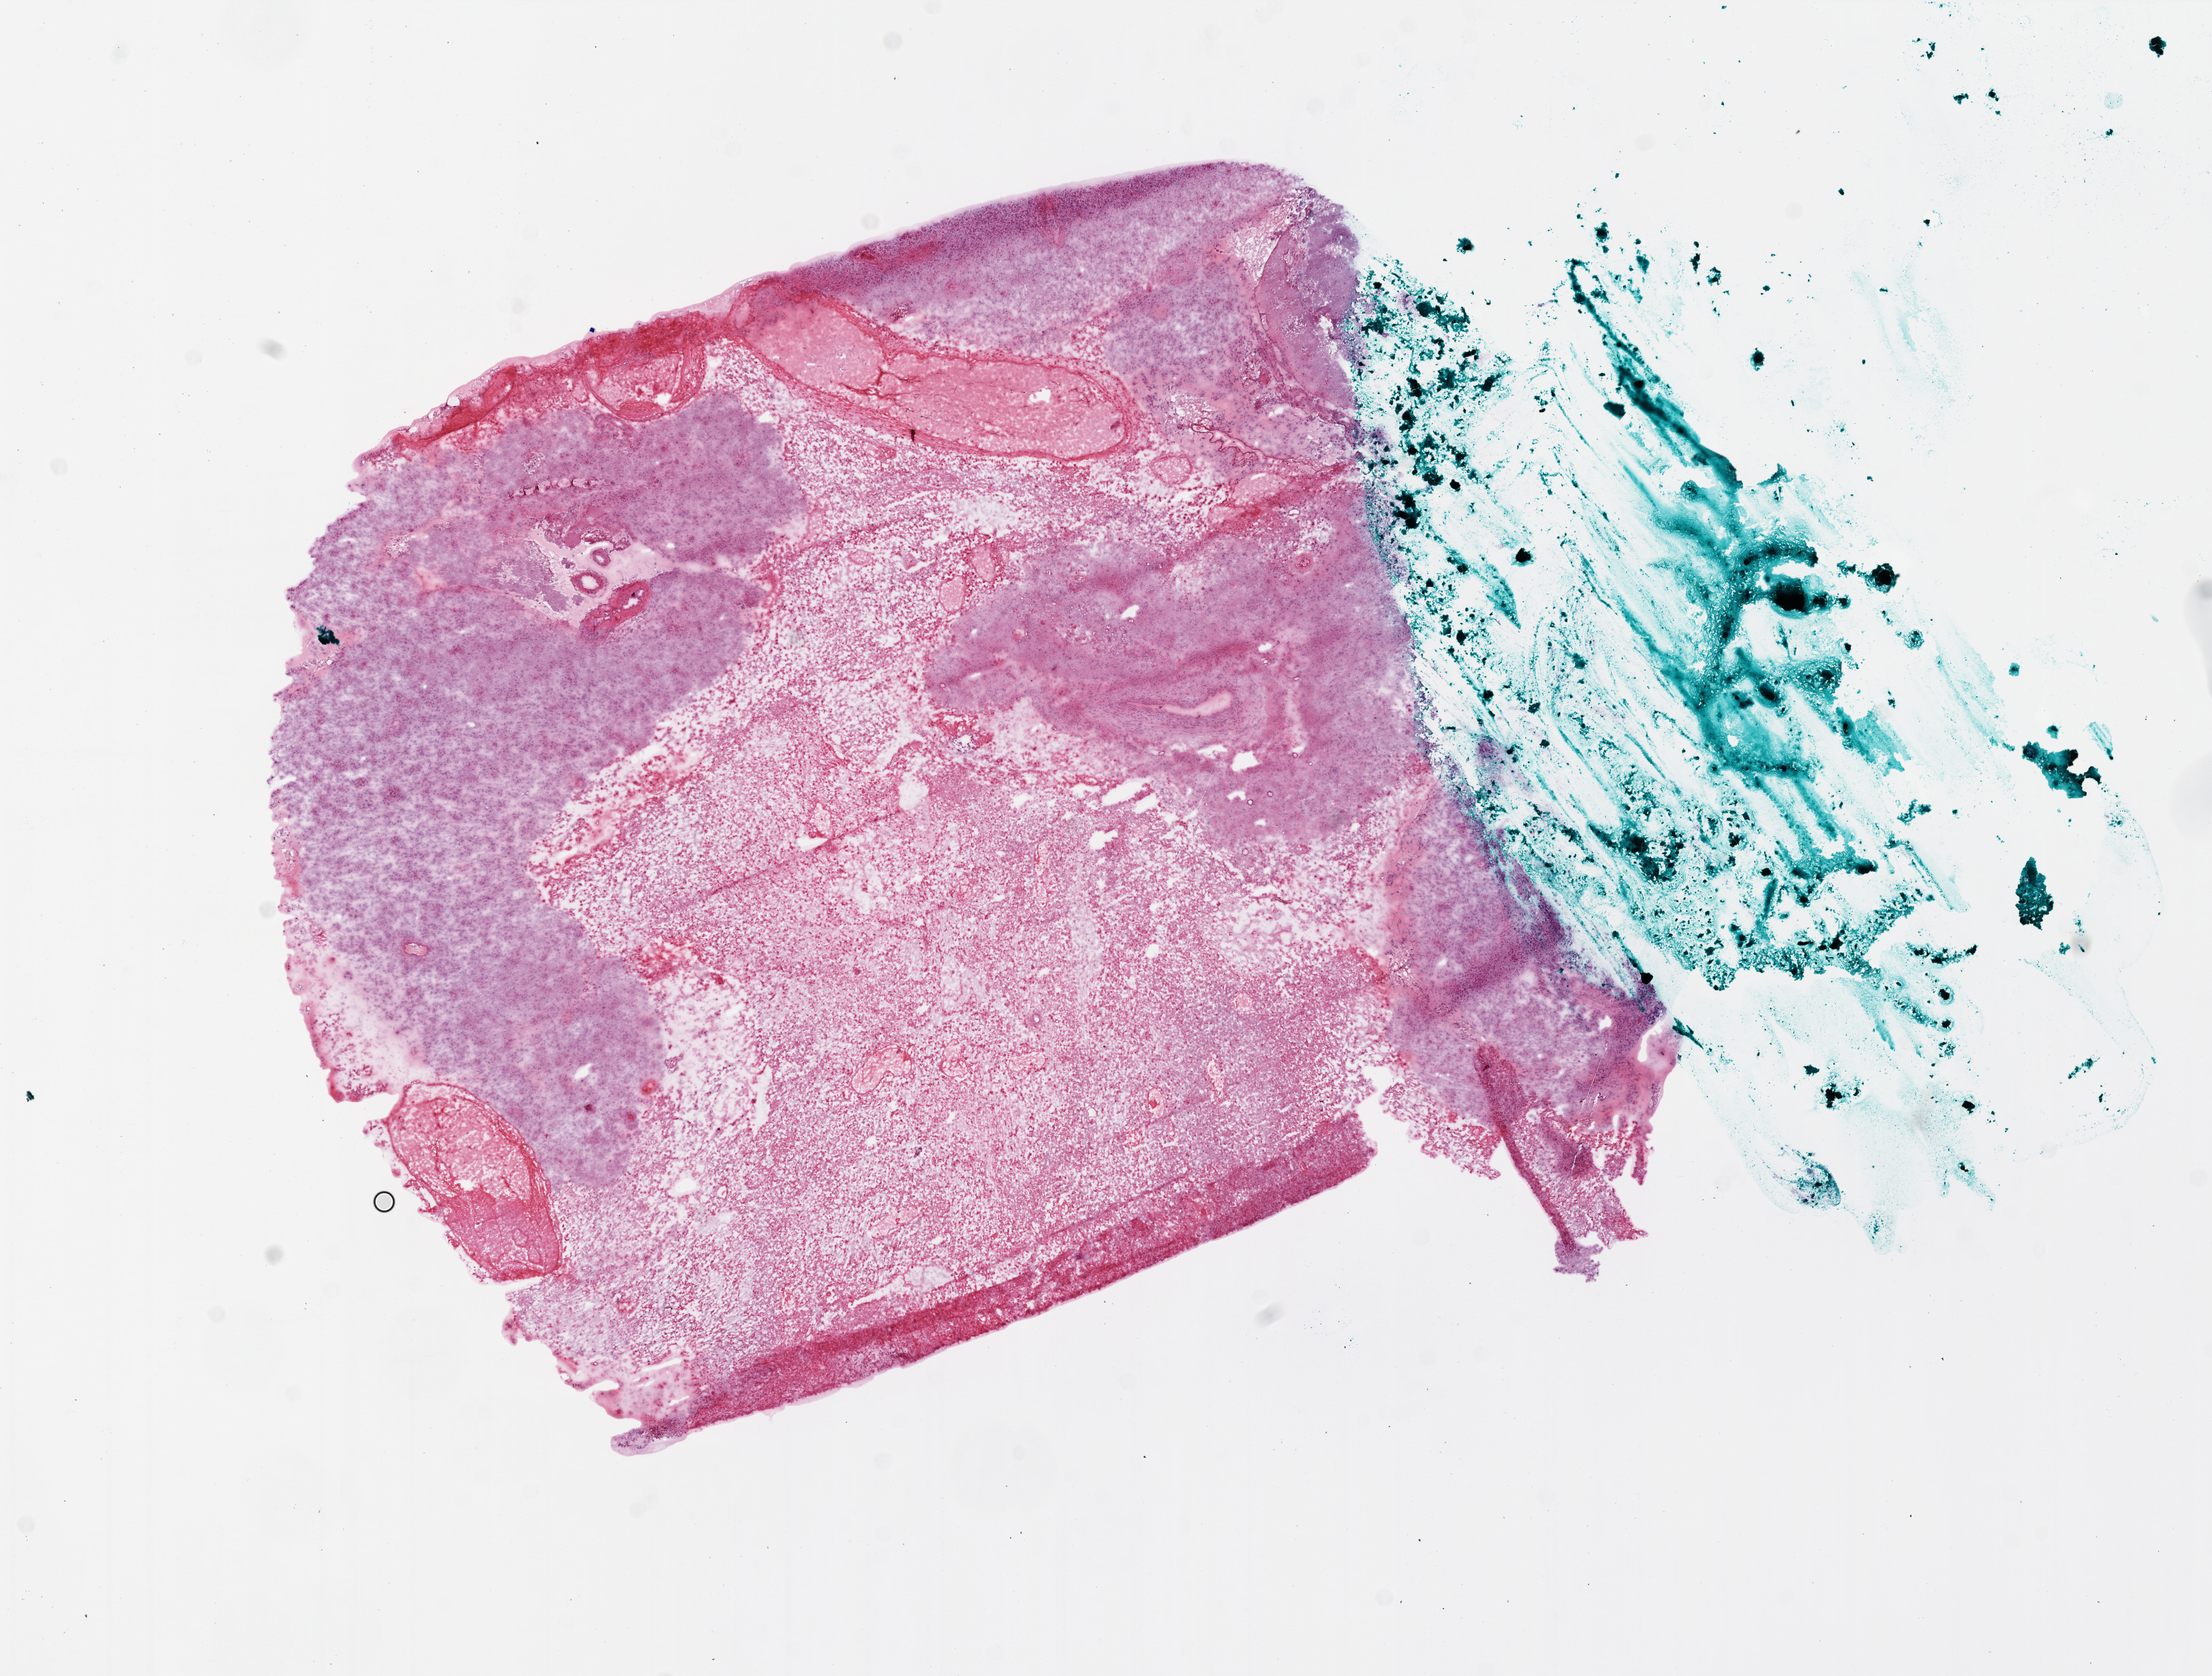
H&E whole-slide image — whole scanned area (about 13.0 x 9.8 mm, from a 20x scan) shown as a low-resolution overview. Frozen section. Brain, primary tumour sample. Male patient; age at initial diagnosis 69 years.
Histologic diagnosis: Glioblastoma.